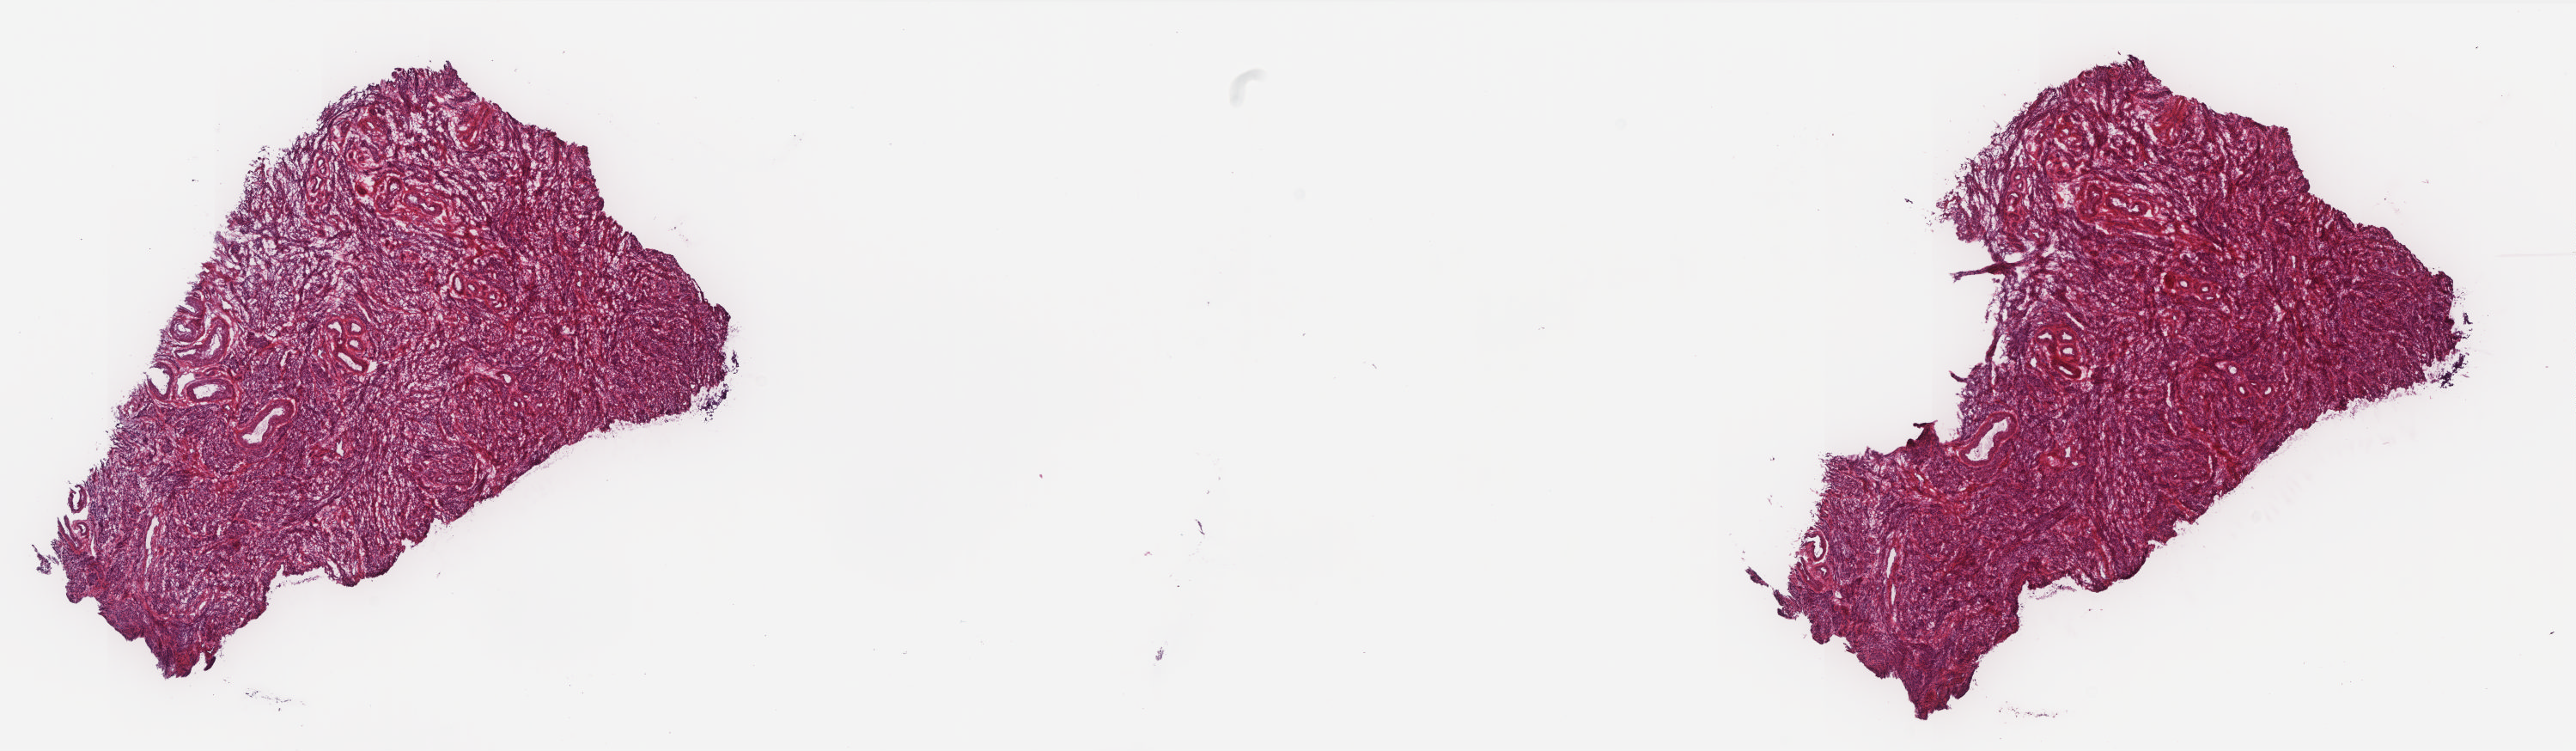
Hematoxylin and eosin (H&E) stained whole-slide image, whole scanned area (about 24.0 x 7.0 mm, acquisition: 20x scan) shown as a low-resolution overview, frozen section from the top of the tissue portion, cervix, solid tissue normal (non-tumour tissue) sample. Patient: female, age at initial diagnosis 55 years. Pathologist review of this section (percent, as recorded): tumour cells 0%, tumour nuclei 0%, normal cells 100%, stromal cells 0%, necrosis 0%. Infiltration values recorded for this section: lymphocyte infiltration 0%, monocyte infiltration 0%, neutrophil infiltration 0%.
- this section: solid tissue normal (non-tumour) sample from the same patient
- patient diagnosis: Adenocarcinoma, NOS